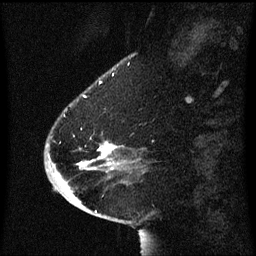
Breast MRI (dynamic contrast-enhanced), one sagittal slice. Position 16 of 60 along the scan axis. Dynamic contrast-enhanced series, image 2 of 3 at this slice position (ordered by acquisition). 1.5 T. TE 4.2 ms, TR 8.4 ms. 2 mm slice thickness. 256 × 256 image matrix, field of view 200 × 200 mm. Patient: female, 54 years. From the clinical record (not read from this slice): setting: breast cancer imaged before/during neoadjuvant chemotherapy; receptor status: HR-positive, HER2-negative.
Outlined on this slice (semi-automatically segmented with operator editing):
- analysis volume of interest (the breast-tissue region the enhancement analysis was run in; not a lesion): bounding box [x1, y1, x2, y2] px = [46, 104, 123, 171]
- tumour enhancement mask (voxels above the 70 % enhancement threshold inside the analysis volume of interest): [101, 146, 116, 155]